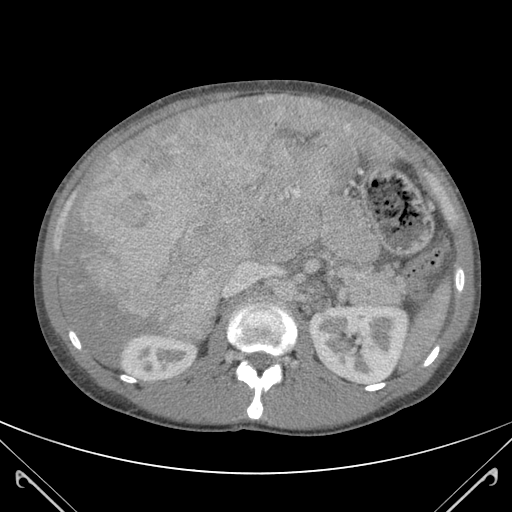
Contrast-enhanced abdominal CT (liver protocol), one axial slice; slice 69 of 118 in the series (ordered by position); soft-tissue window (W 400 / L 40 HU); 3 mm slice thickness; 512 × 512 image matrix, field of view 380 × 380 mm. From the clinical record (not read from this slice): diagnosis: hepatocellular carcinoma (patient treated with transarterial chemoembolisation; whether this scan precedes or follows treatment is not stated here); TNM stage (as recorded): Stage-IIIB; Child-Pugh class: A; tumour nodularity: uninodular.
Outlined on this slice (semi-automatically segmented with operator editing):
- abdominal aorta: bounding box (x1, y1, x2, y2) in pixels: (276, 279, 298, 302)
- liver parenchyma outside the tumour (the mass and vessels are separate outlines, so this box may not span the whole liver): (58, 96, 382, 362)
- mass: (64, 96, 369, 338)
- liver vessels: (222, 97, 362, 297)